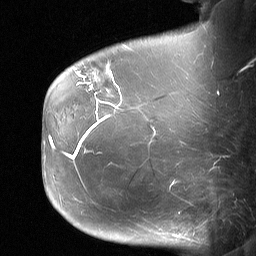
Breast MRI (dynamic contrast-enhanced), one sagittal slice; slice 17 of 64 in the series (ordered by position); dynamic contrast-enhanced study with each time point stored as its own series, time point 2 of 3 at this slice position (early post-contrast, ordered by acquisition time); 1.5 T; TE 4.8 ms, TR 27 ms; 2 mm slice thickness; 256 × 256 image matrix, field of view 200 × 200 mm. Female patient, age 60 years. Case-level facts recorded for this patient, not image findings: setting: breast cancer imaged before/during neoadjuvant chemotherapy; receptor status: HR-positive, HER2-negative.
Annotated regions visible in this slice (semi-automatically segmented with operator editing):
- analysis volume of interest (the breast-tissue region the enhancement analysis was run in; not a lesion): bounding box [x1, y1, x2, y2] px = [79, 50, 122, 99]
- tumour enhancement mask (voxels above the 90 % enhancement threshold inside the analysis volume of interest): [87, 66, 109, 95]